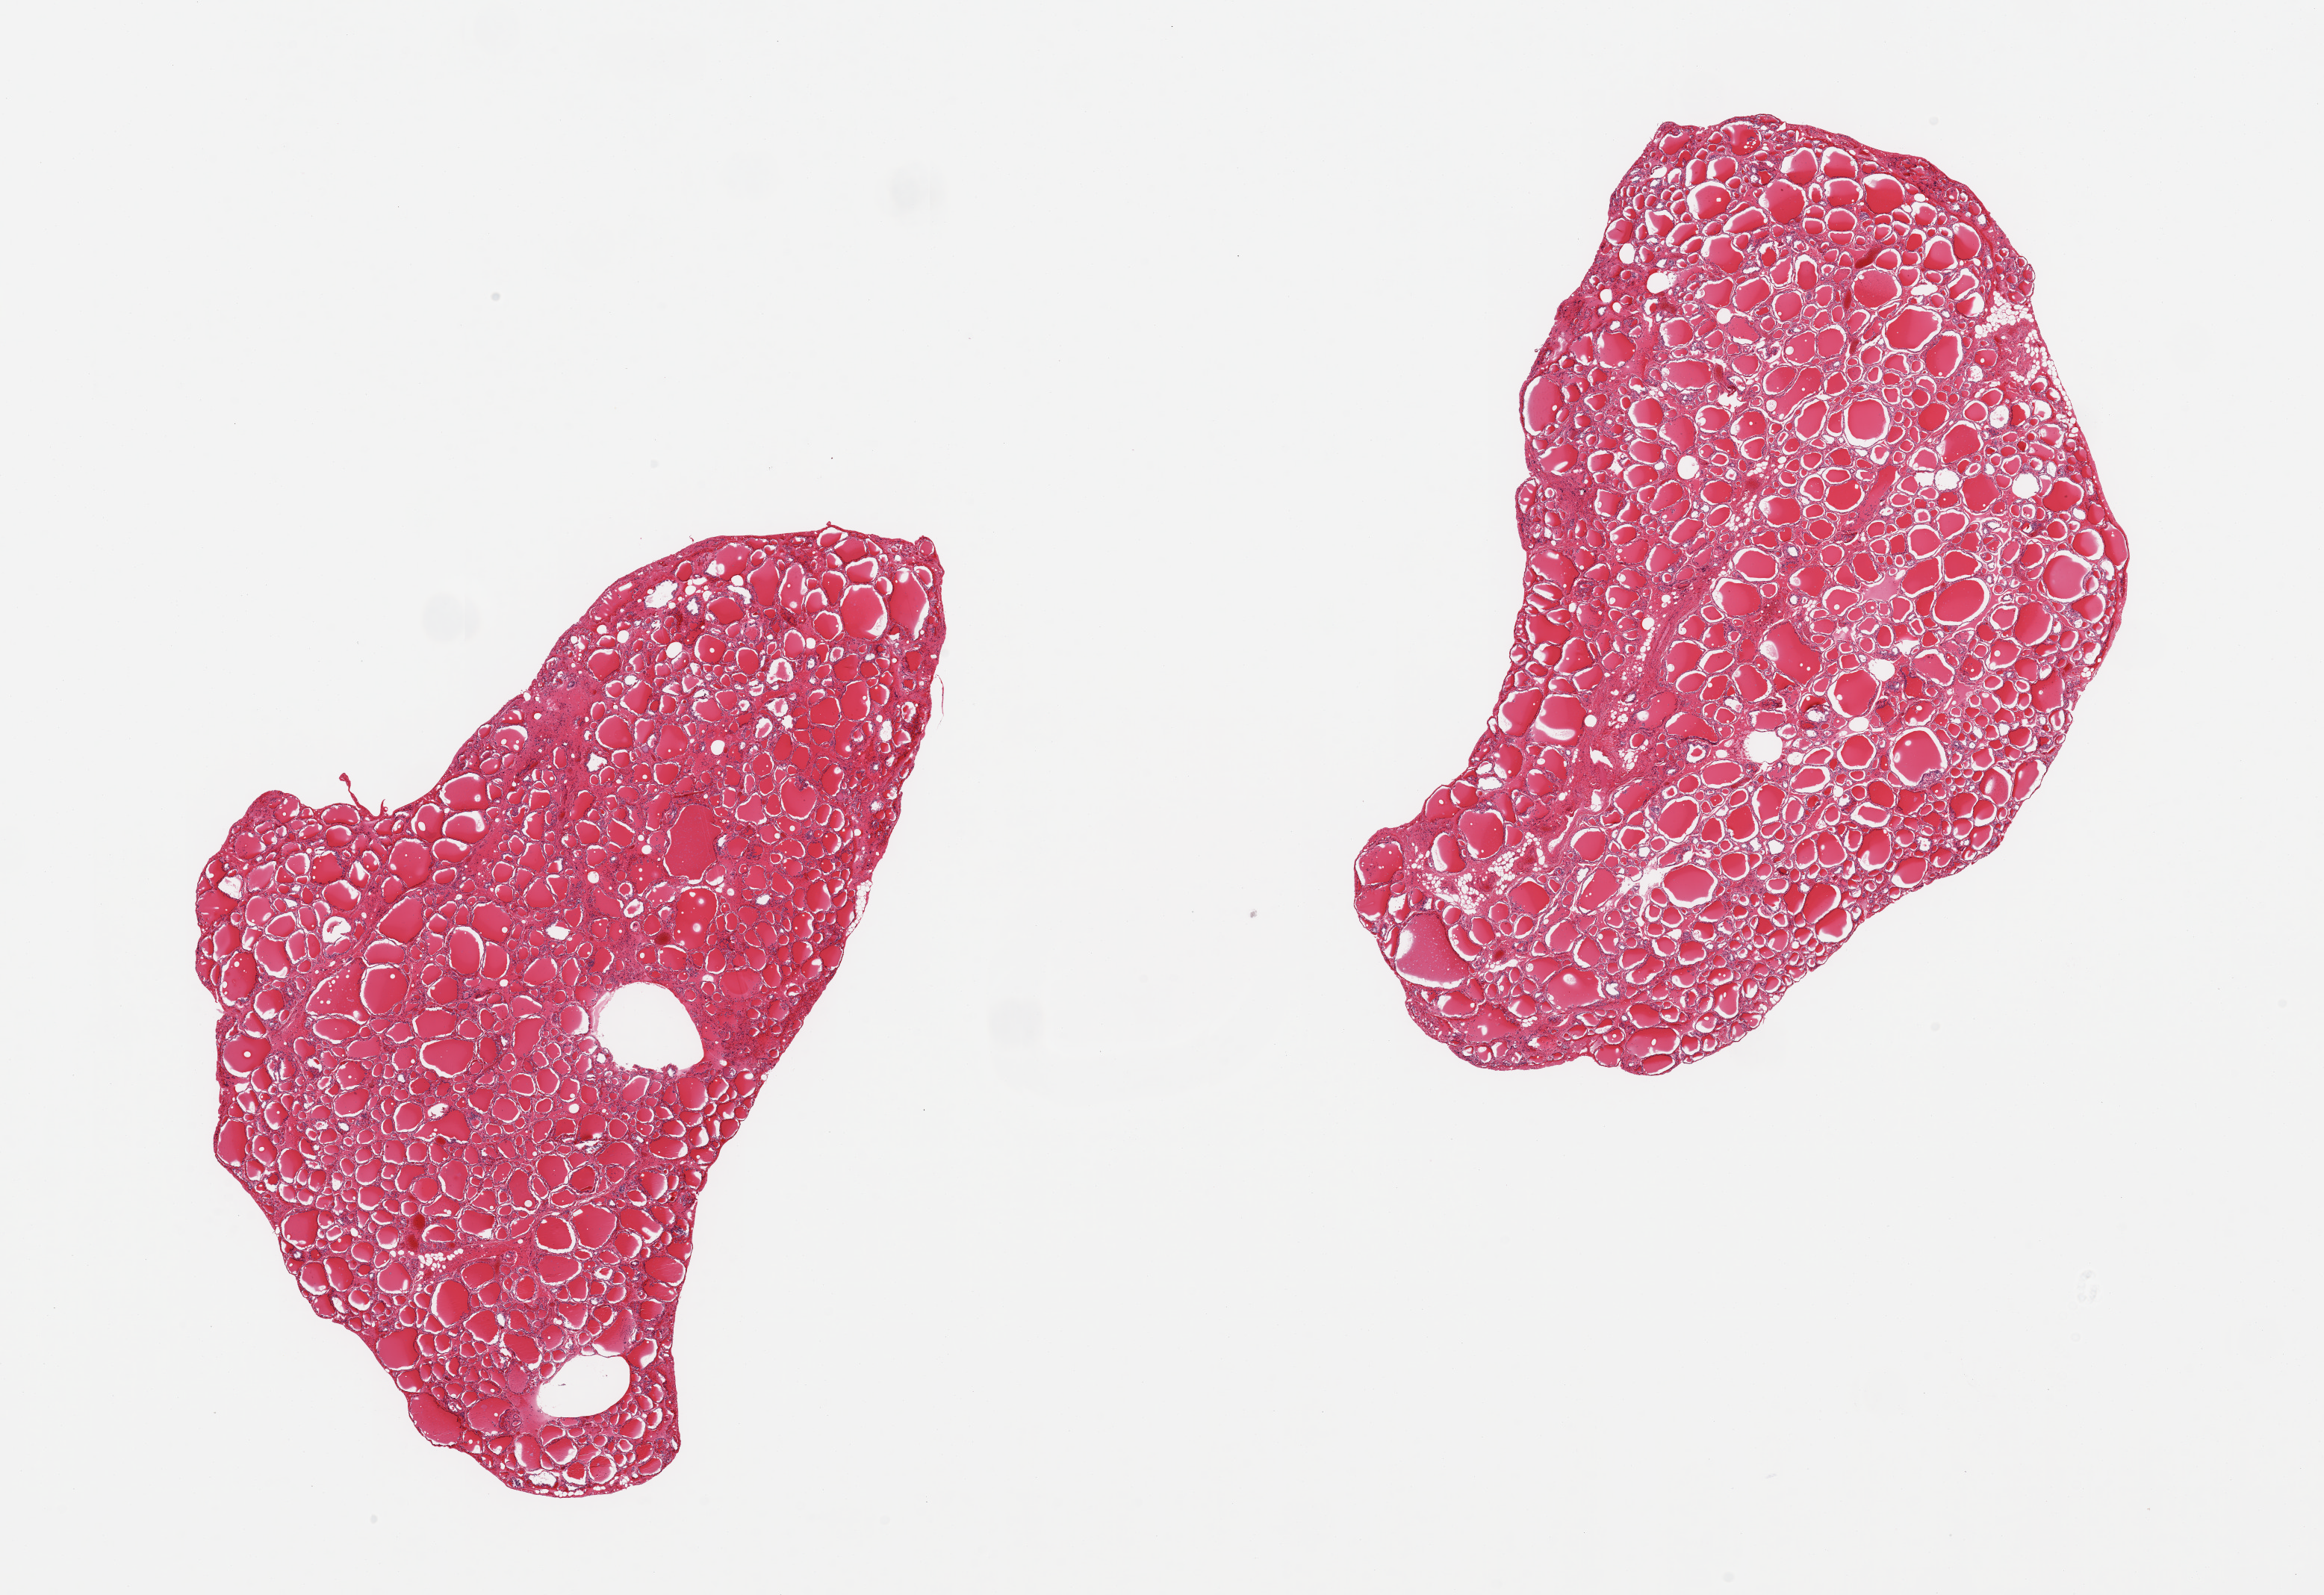
Digitized haematoxylin and eosin-stained section, brightfield, whole scanned area (about 24.6 x 16.9 mm, from a 20x scan) shown as a low-resolution overview; PAXgene-fixed paraffin-embedded (PFPE) section; sampled site (target tissue): thyroid; donor tissue sample. Donor: male.
Pathologist's review note for this sample: 2 pieces, no abnormalities.